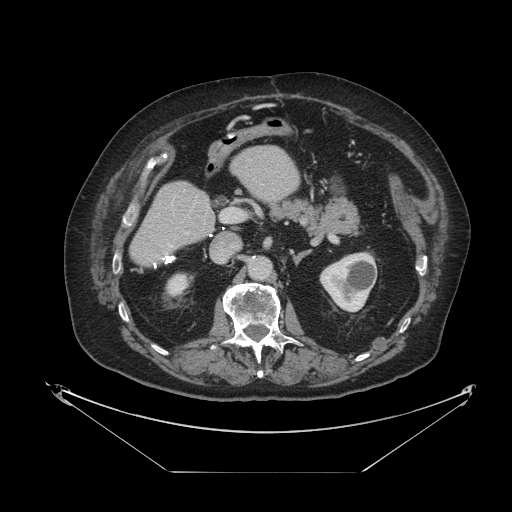
Contrast-enhanced abdominal CT, one axial slice. 120 kVp. Intravenous contrast given. Soft-tissue window (W 400 / L 40 HU). 2.5 mm slice thickness. 512 × 512 image matrix, field of view 500 × 500 mm. Male patient, age 68 years. From the clinical record (not read from this slice): diagnosis: colorectal cancer liver metastases, imaged before liver resection; multiple liver metastases: no.
Outlined on this slice (outlined manually by an expert reader):
- liver: box from (x=131, y=147) to (x=299, y=266) px
- planned liver remnant (the part of the liver to remain after resection): (x=131, y=147)–(x=299, y=266)
- portal vein (with intrahepatic branches): (x=184, y=208)–(x=237, y=234)